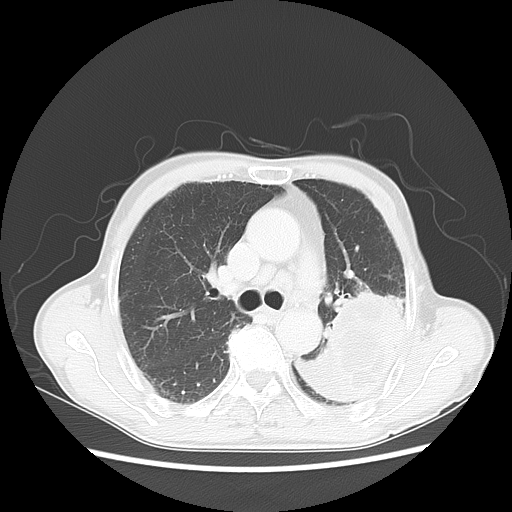
Chest CT, one axial slice. Reconstruction kernel LUNG. 120 kVp. Lung window (W 1500 / L -600 HU). 5 mm slice thickness. 512 × 512 image matrix, field of view 360 × 360 mm. Patient: male, 64 years. From the clinical record (not read from this slice): clinical TNM (as recorded): T4 N0 M0.
Annotated regions visible in this slice (rectangle marked by the reading radiologist):
- lung tumour (recorded histology: squamous cell carcinoma): bounding box <300,276,407,412> (left, top, right, bottom; pixels)